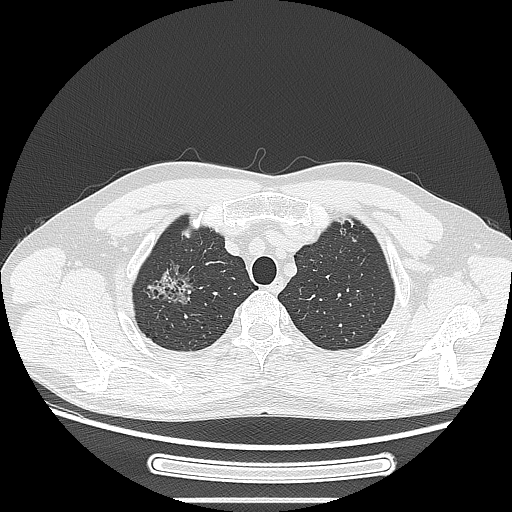
Chest CT, one axial slice; slice 224 of 269 in the series (ordered by position); 120 kVp; lung window (W 1500 / L -600 HU); 512 × 512 image matrix, field of view 382 × 382 mm. Male patient, age 53 years. From the clinical record (not read from this slice): clinical TNM (as recorded): T1c N0 M0; histopathological grade: G2.
Annotated regions visible in this slice (bounding box drawn by a radiologist):
- lung tumour (recorded histology: adenocarcinoma): bounding box (x1, y1, x2, y2) in pixels: (145, 261, 195, 314)